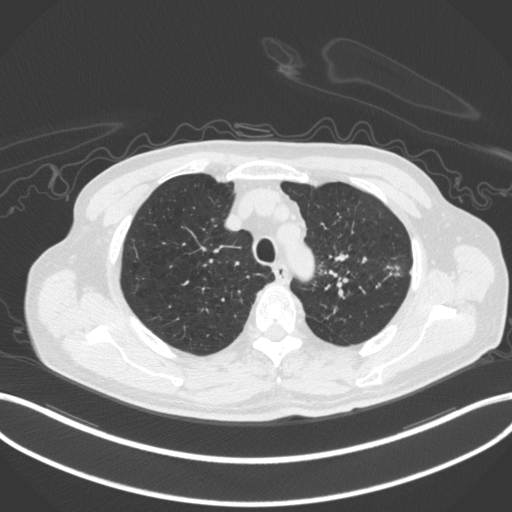
Chest CT, one axial slice. Slice 351 of 420 in the series (ordered by position). Reconstruction kernel B31f. 120 kVp. Lung window (W 1500 / L -600 HU). 1 mm slice thickness. 512 × 512 image matrix. Male patient, age 77 years. From the clinical record (not read from this slice): clinical TNM (as recorded): T3 N1 M0.
Annotated regions visible in this slice (bounding box drawn by a radiologist):
- lung tumour (recorded histology: adenocarcinoma): bounding box <383,262,405,279> (left, top, right, bottom; pixels)